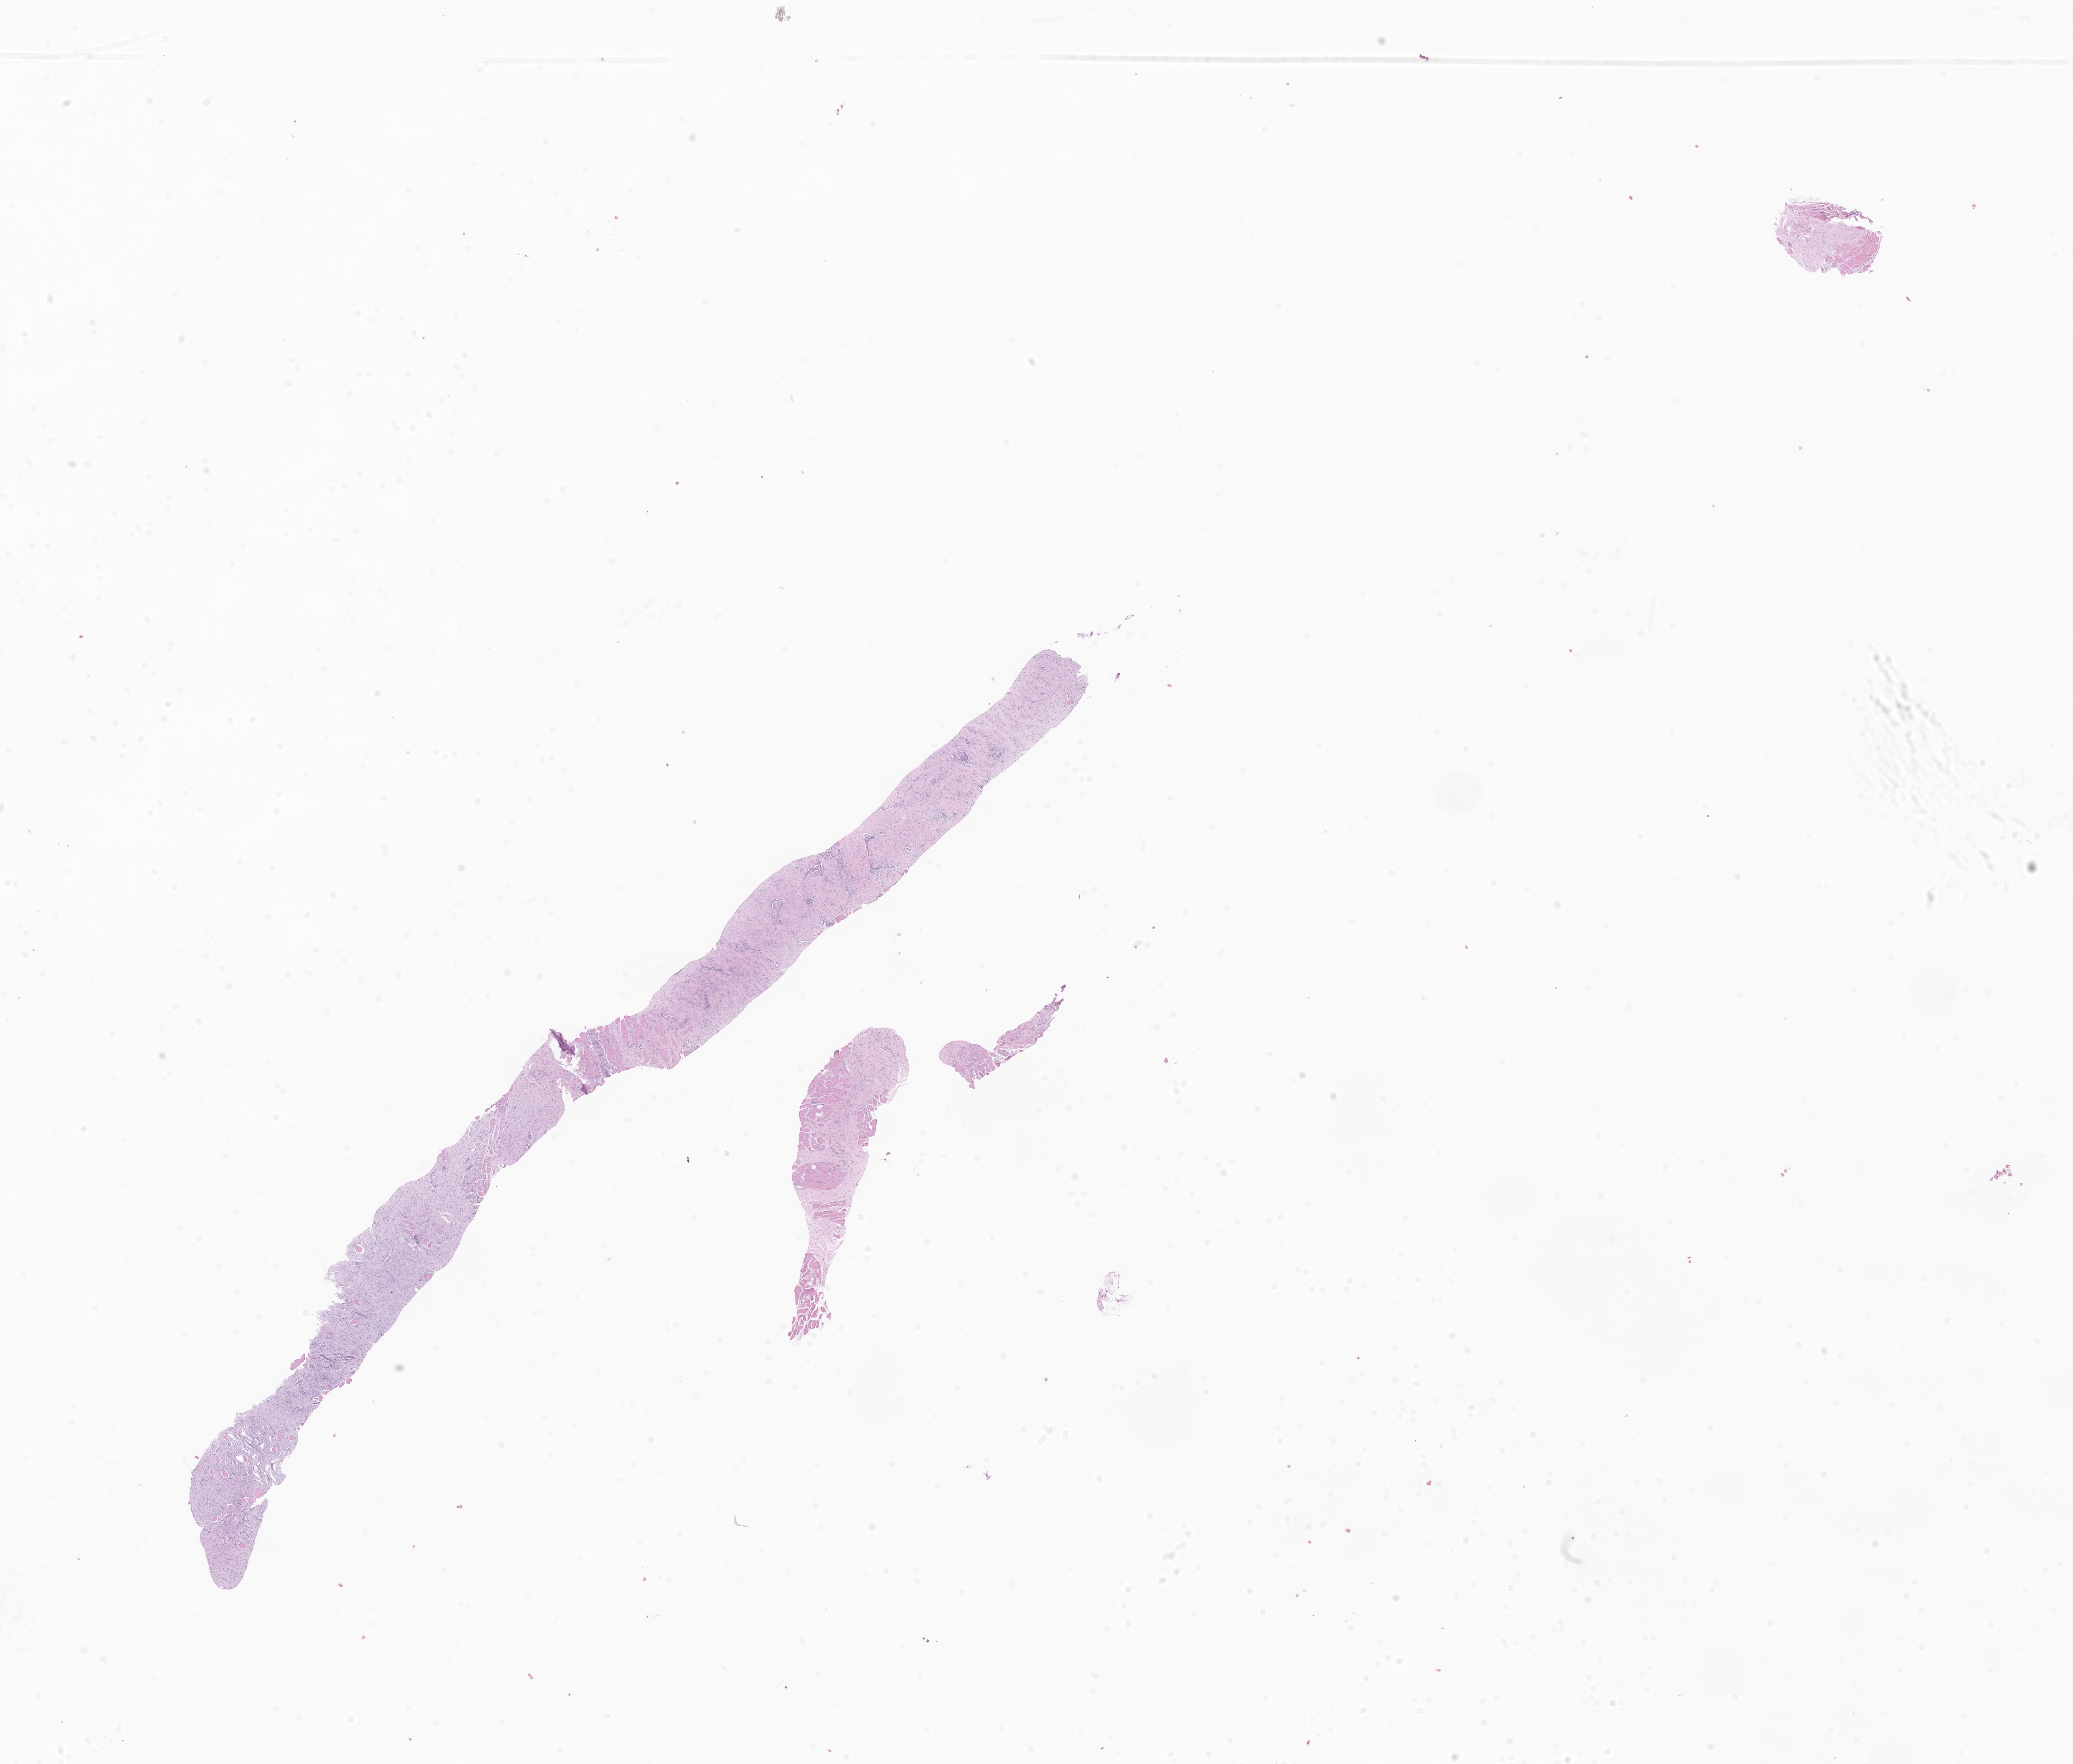
Whole-slide image, haematoxylin and eosin stain of tumor tissue from the soft tissue, shown as a low-resolution overview of the whole scanned area (about 21.6 x 18.4 mm). FFPE section. Patient female; age 151 months (12 years 7 months).
Diagnosis: Aggressive fibromatosis.